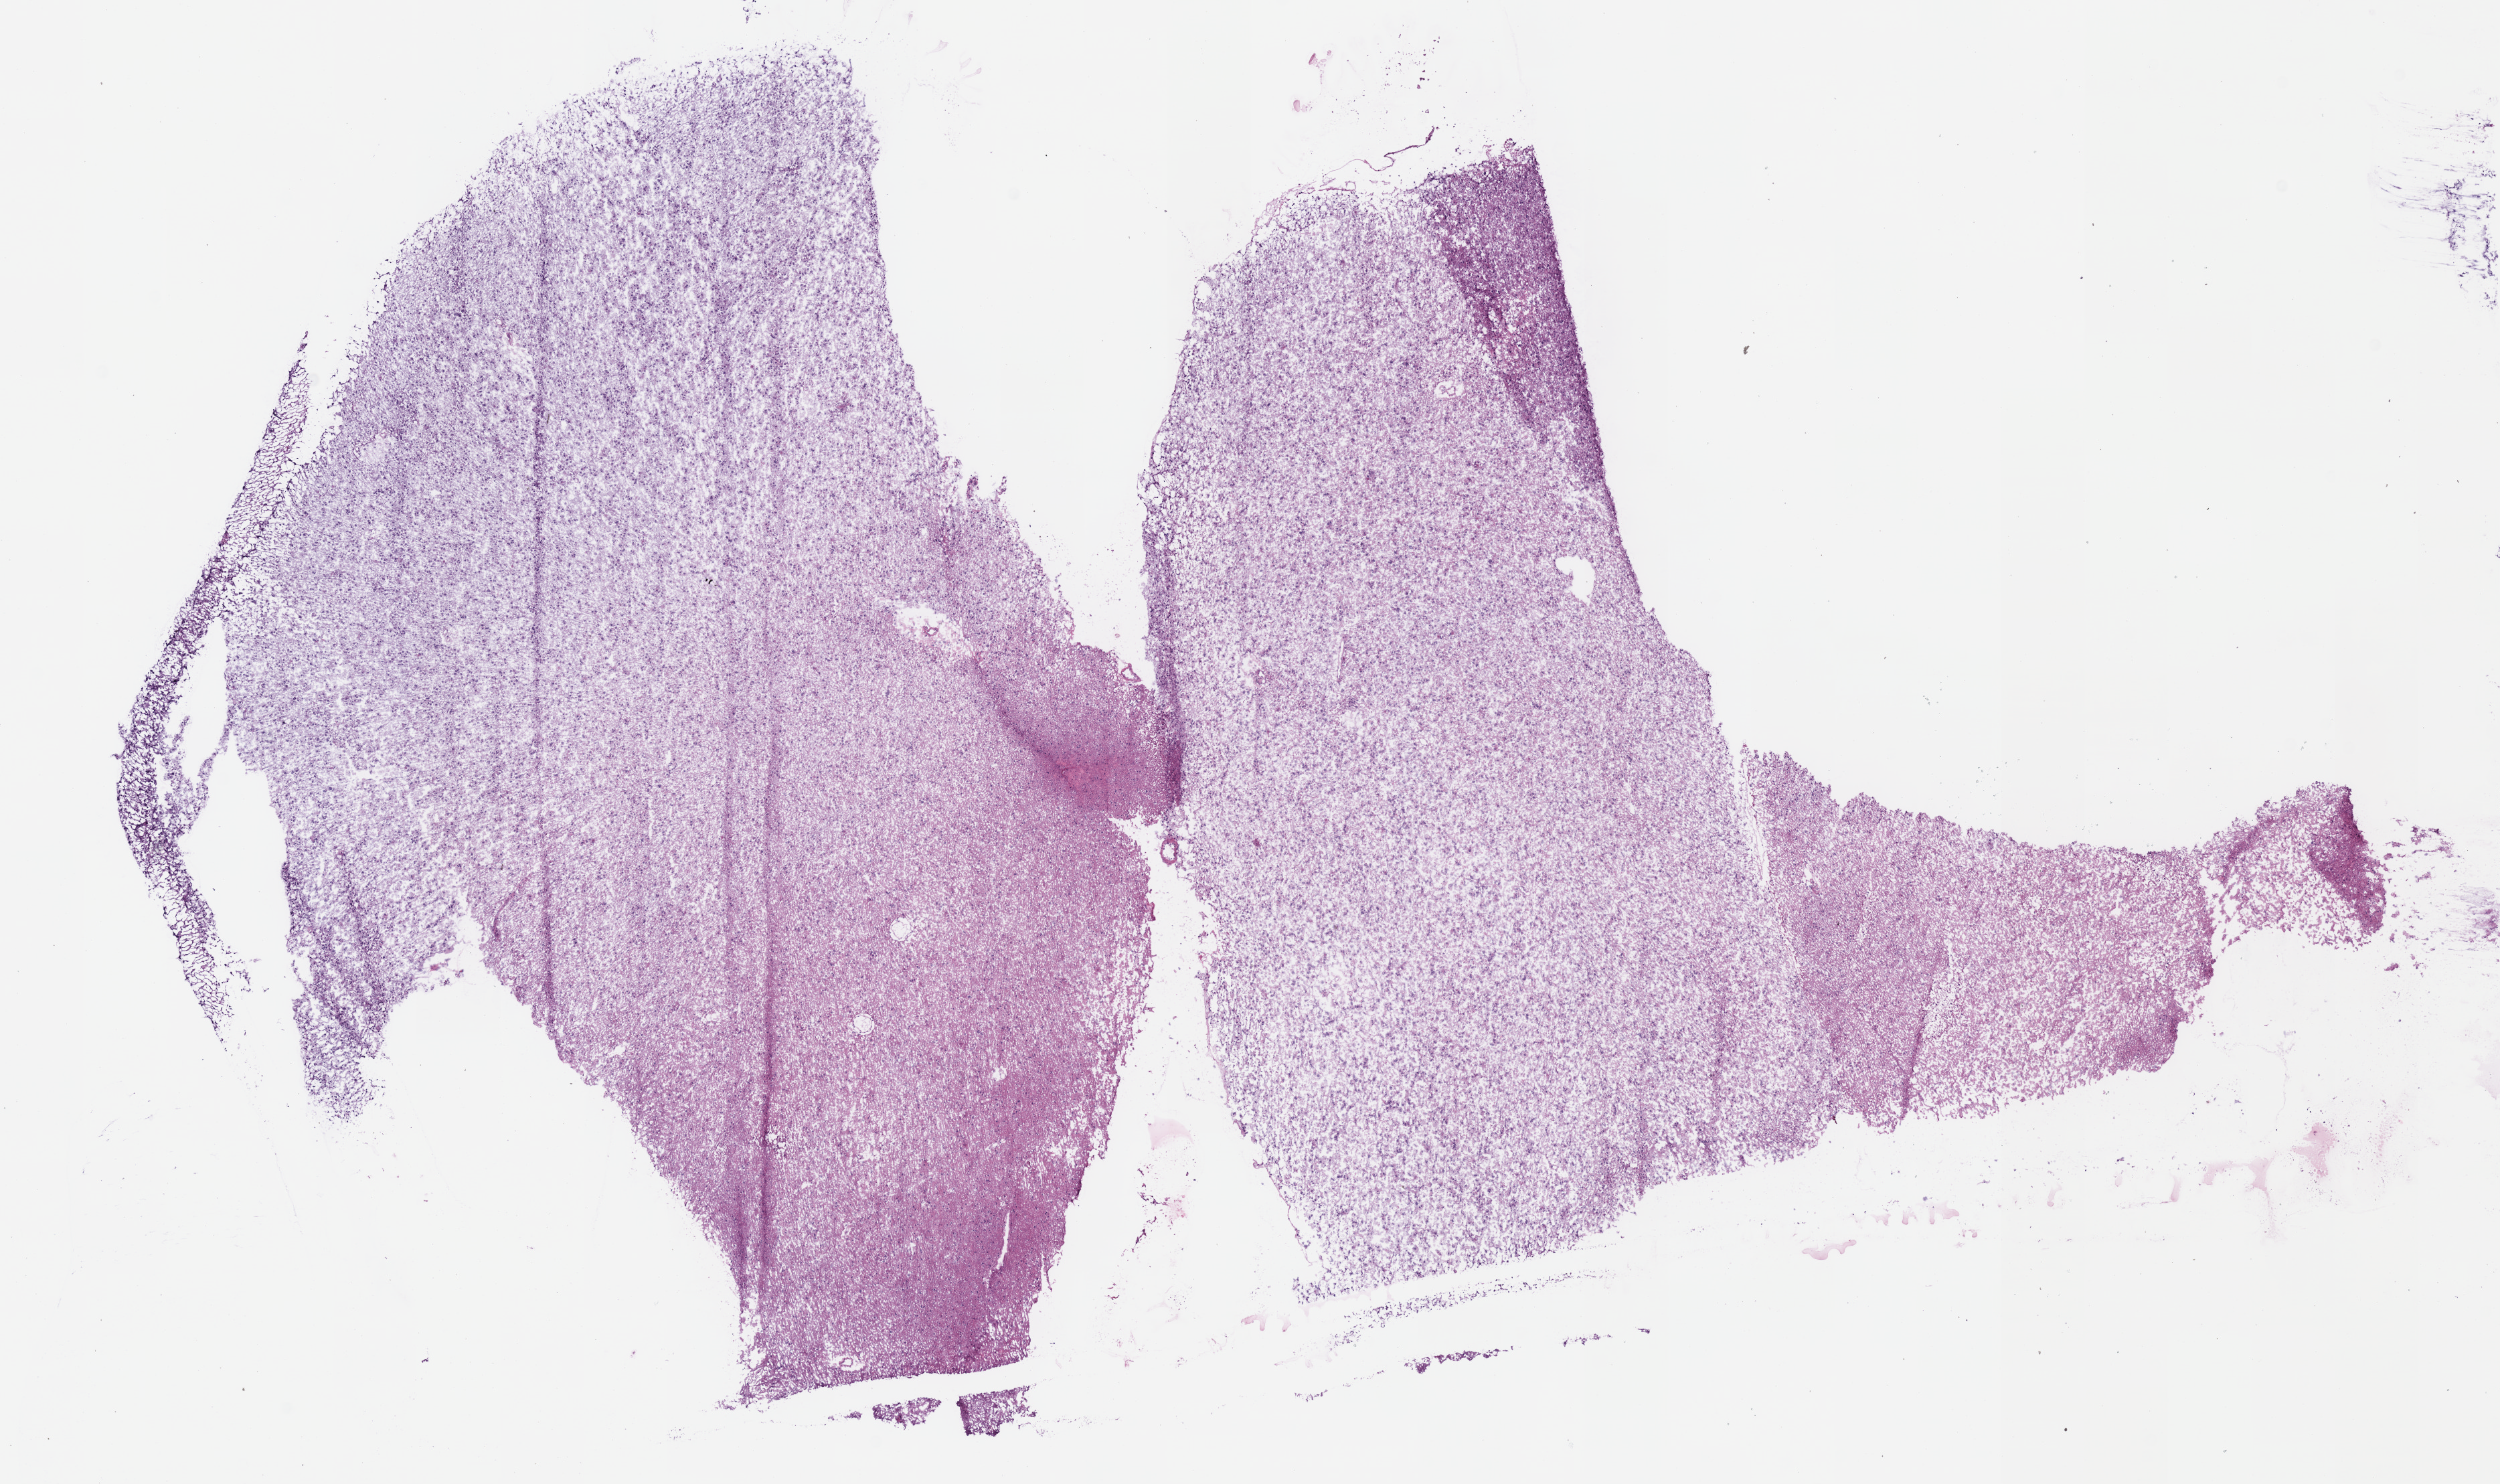
Digitized H&E tissue section (whole slide), whole scanned area (about 14.7 x 8.7 mm) shown as a low-resolution overview; frozen section; primary tumour sample from the brain. Patient: female, age at initial diagnosis 44 years. Histologic grade: G2 (moderately differentiated). Pathologist review of this section (percent, as recorded): tumour cells 100%, tumour nuclei 70%, normal cells 0%, stromal cells 0%, necrosis 0%.
Diagnosis: Astrocytoma, NOS.